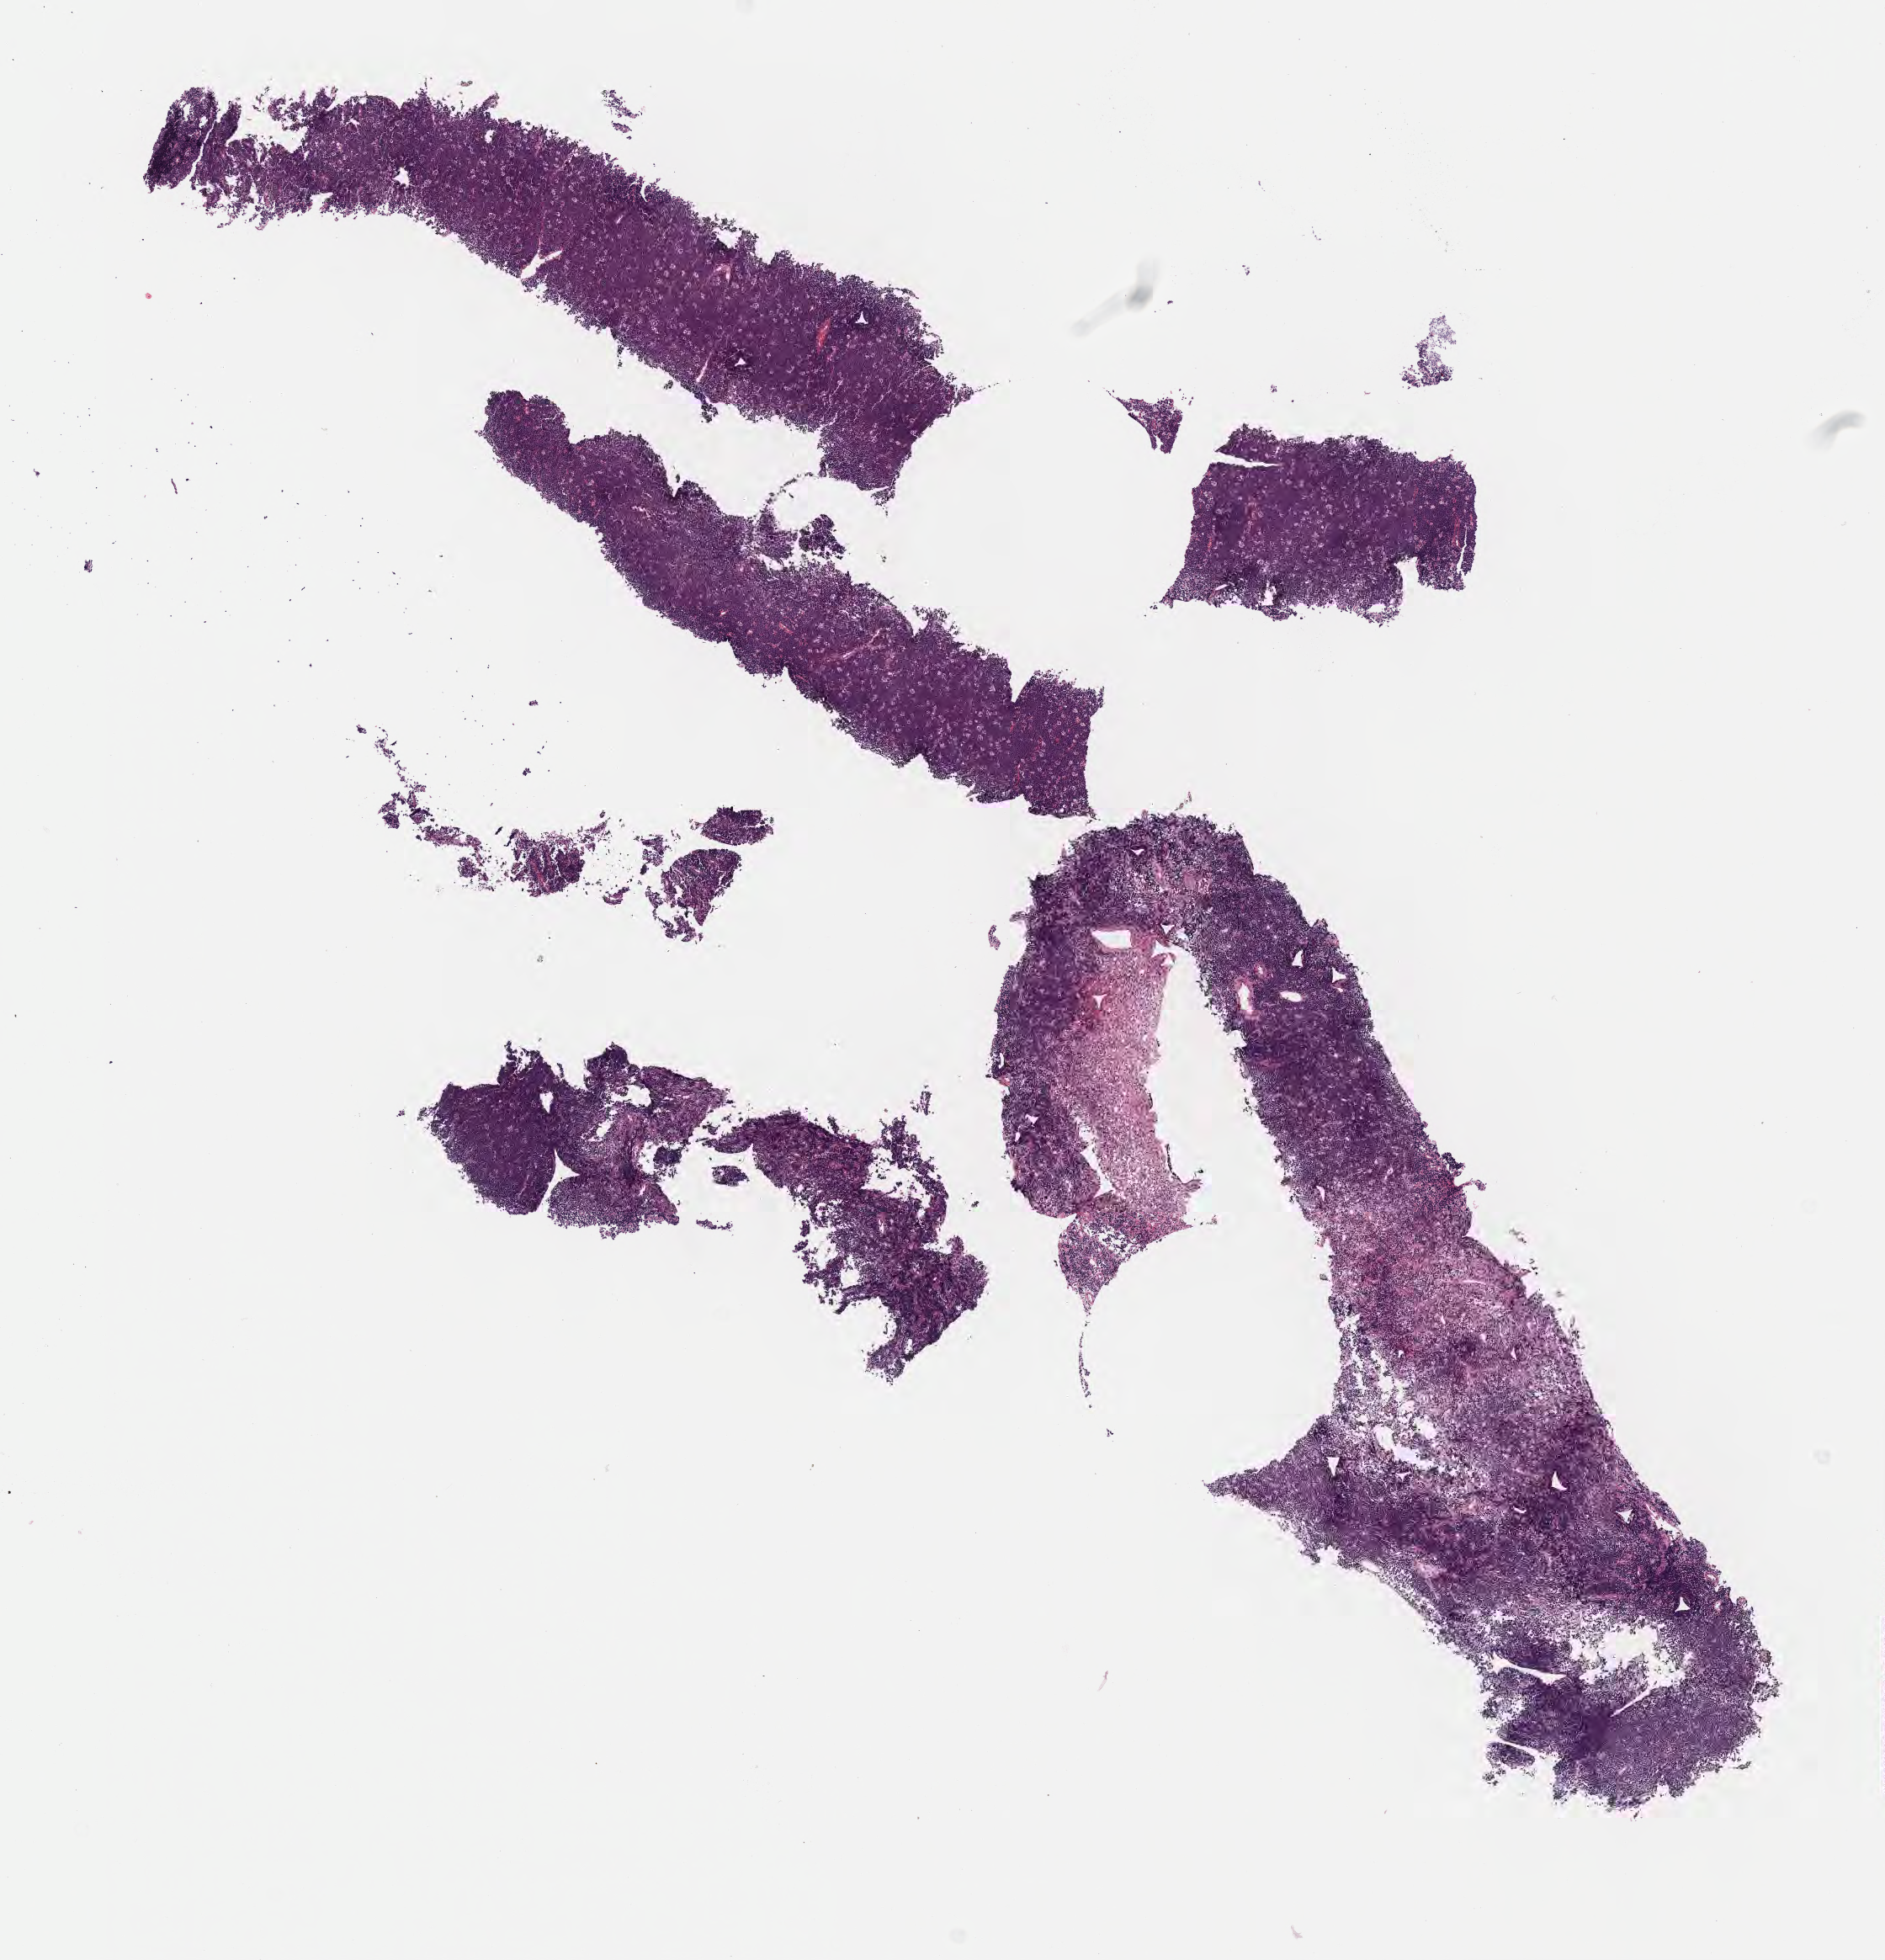
Whole-slide image, H&E stain, shown as a low-resolution overview of the whole scanned area (about 9.1 x 9.4 mm). Specimen: tumor tissue. Site: liver. Male patient; age at initial diagnosis 4 years.
* histologic diagnosis: Burkitt lymphoma, NOS